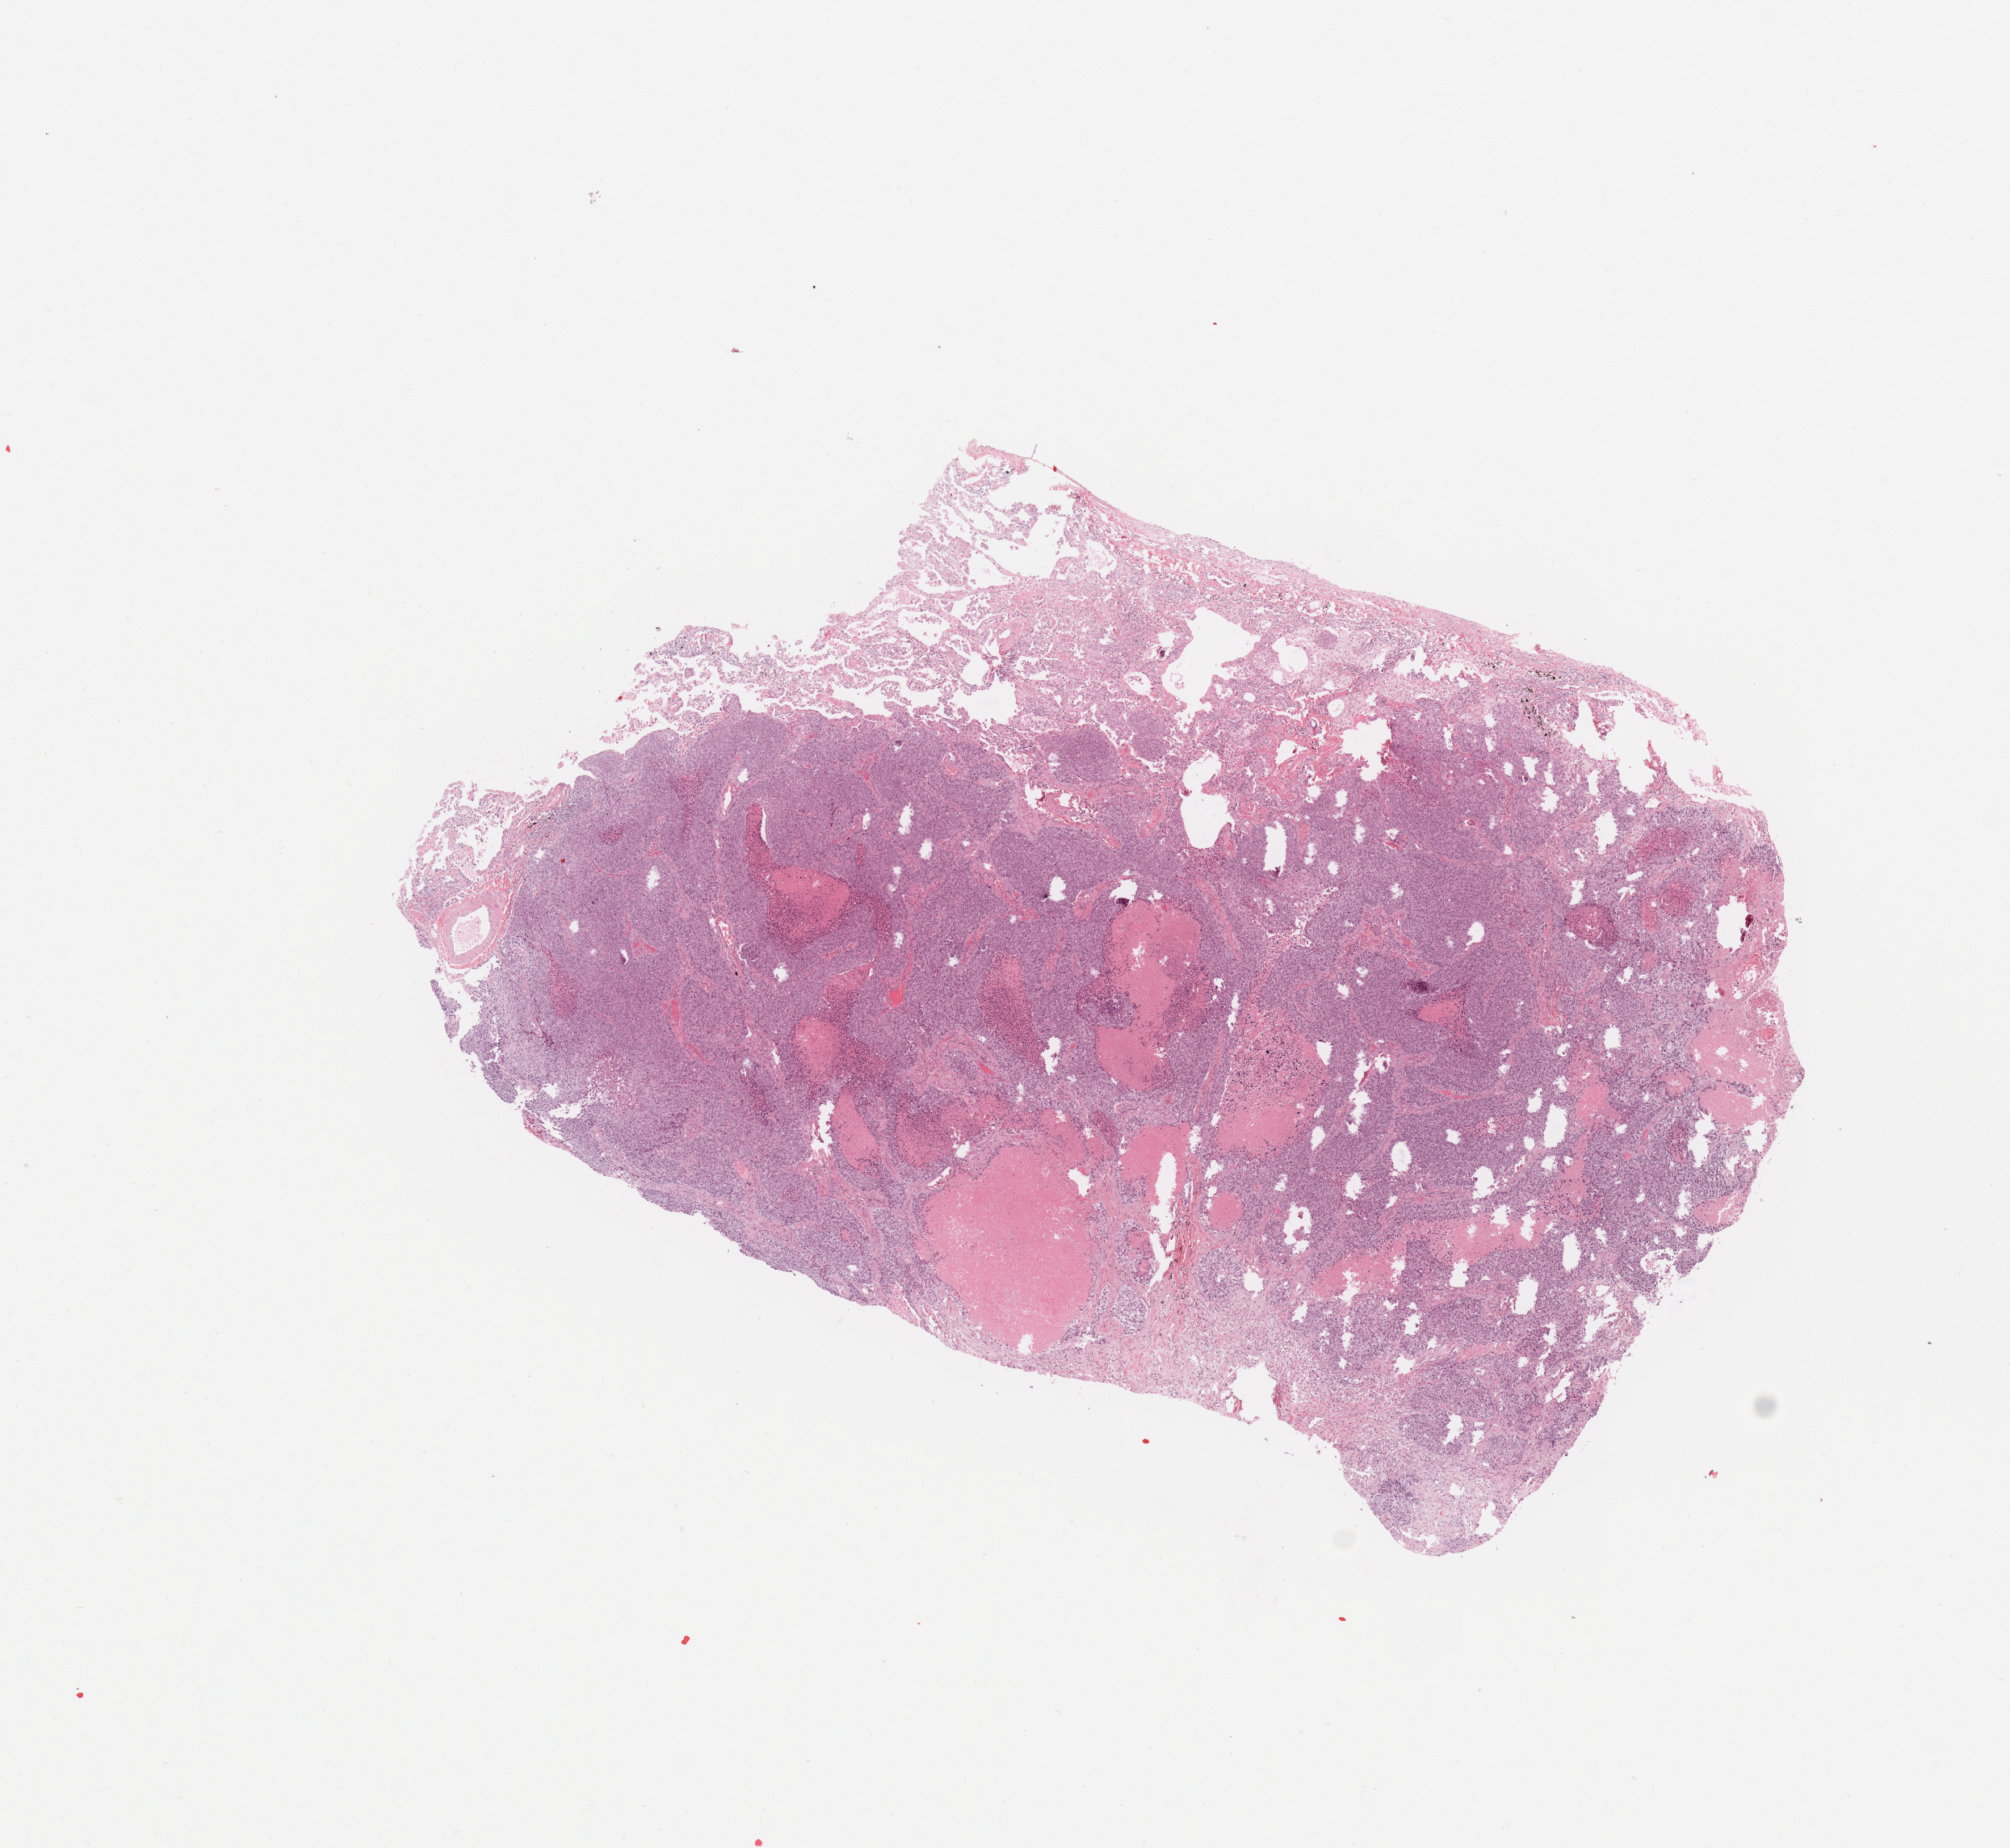
Whole-slide histology image, H&E — low-resolution overview of the scanned area, about 9.8 x 9.0 mm. Tumour tissue sample, sampled site: lung. Male, 53 y/o. Histologic grade: G3 (poorly differentiated). Composition of this section per pathologist review: tumour nuclei 70%, necrosis 20%.
AJCC pathologic stage: IIIB. Primary tumour site (as recorded): right lower lobe. Histologic diagnosis: Squamous cell carcinoma, NOS.